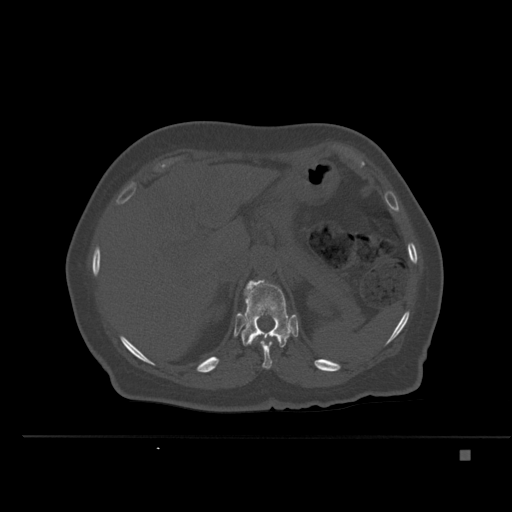
CT including the spine, one axial slice. Bone window (W 1800 / L 400 HU). 1.5 mm slice thickness. 512 × 512 image matrix, field of view 422 × 422 mm. Female patient, age 74 years. Case-level facts recorded for this patient, not image findings: primary cancer: colon.
Outlined on this slice (semi-automatically segmented with operator editing):
- T11 vertebra: bounding box <251,336,279,369> (left, top, right, bottom; pixels)
- T12 vertebra: <241,279,290,347>